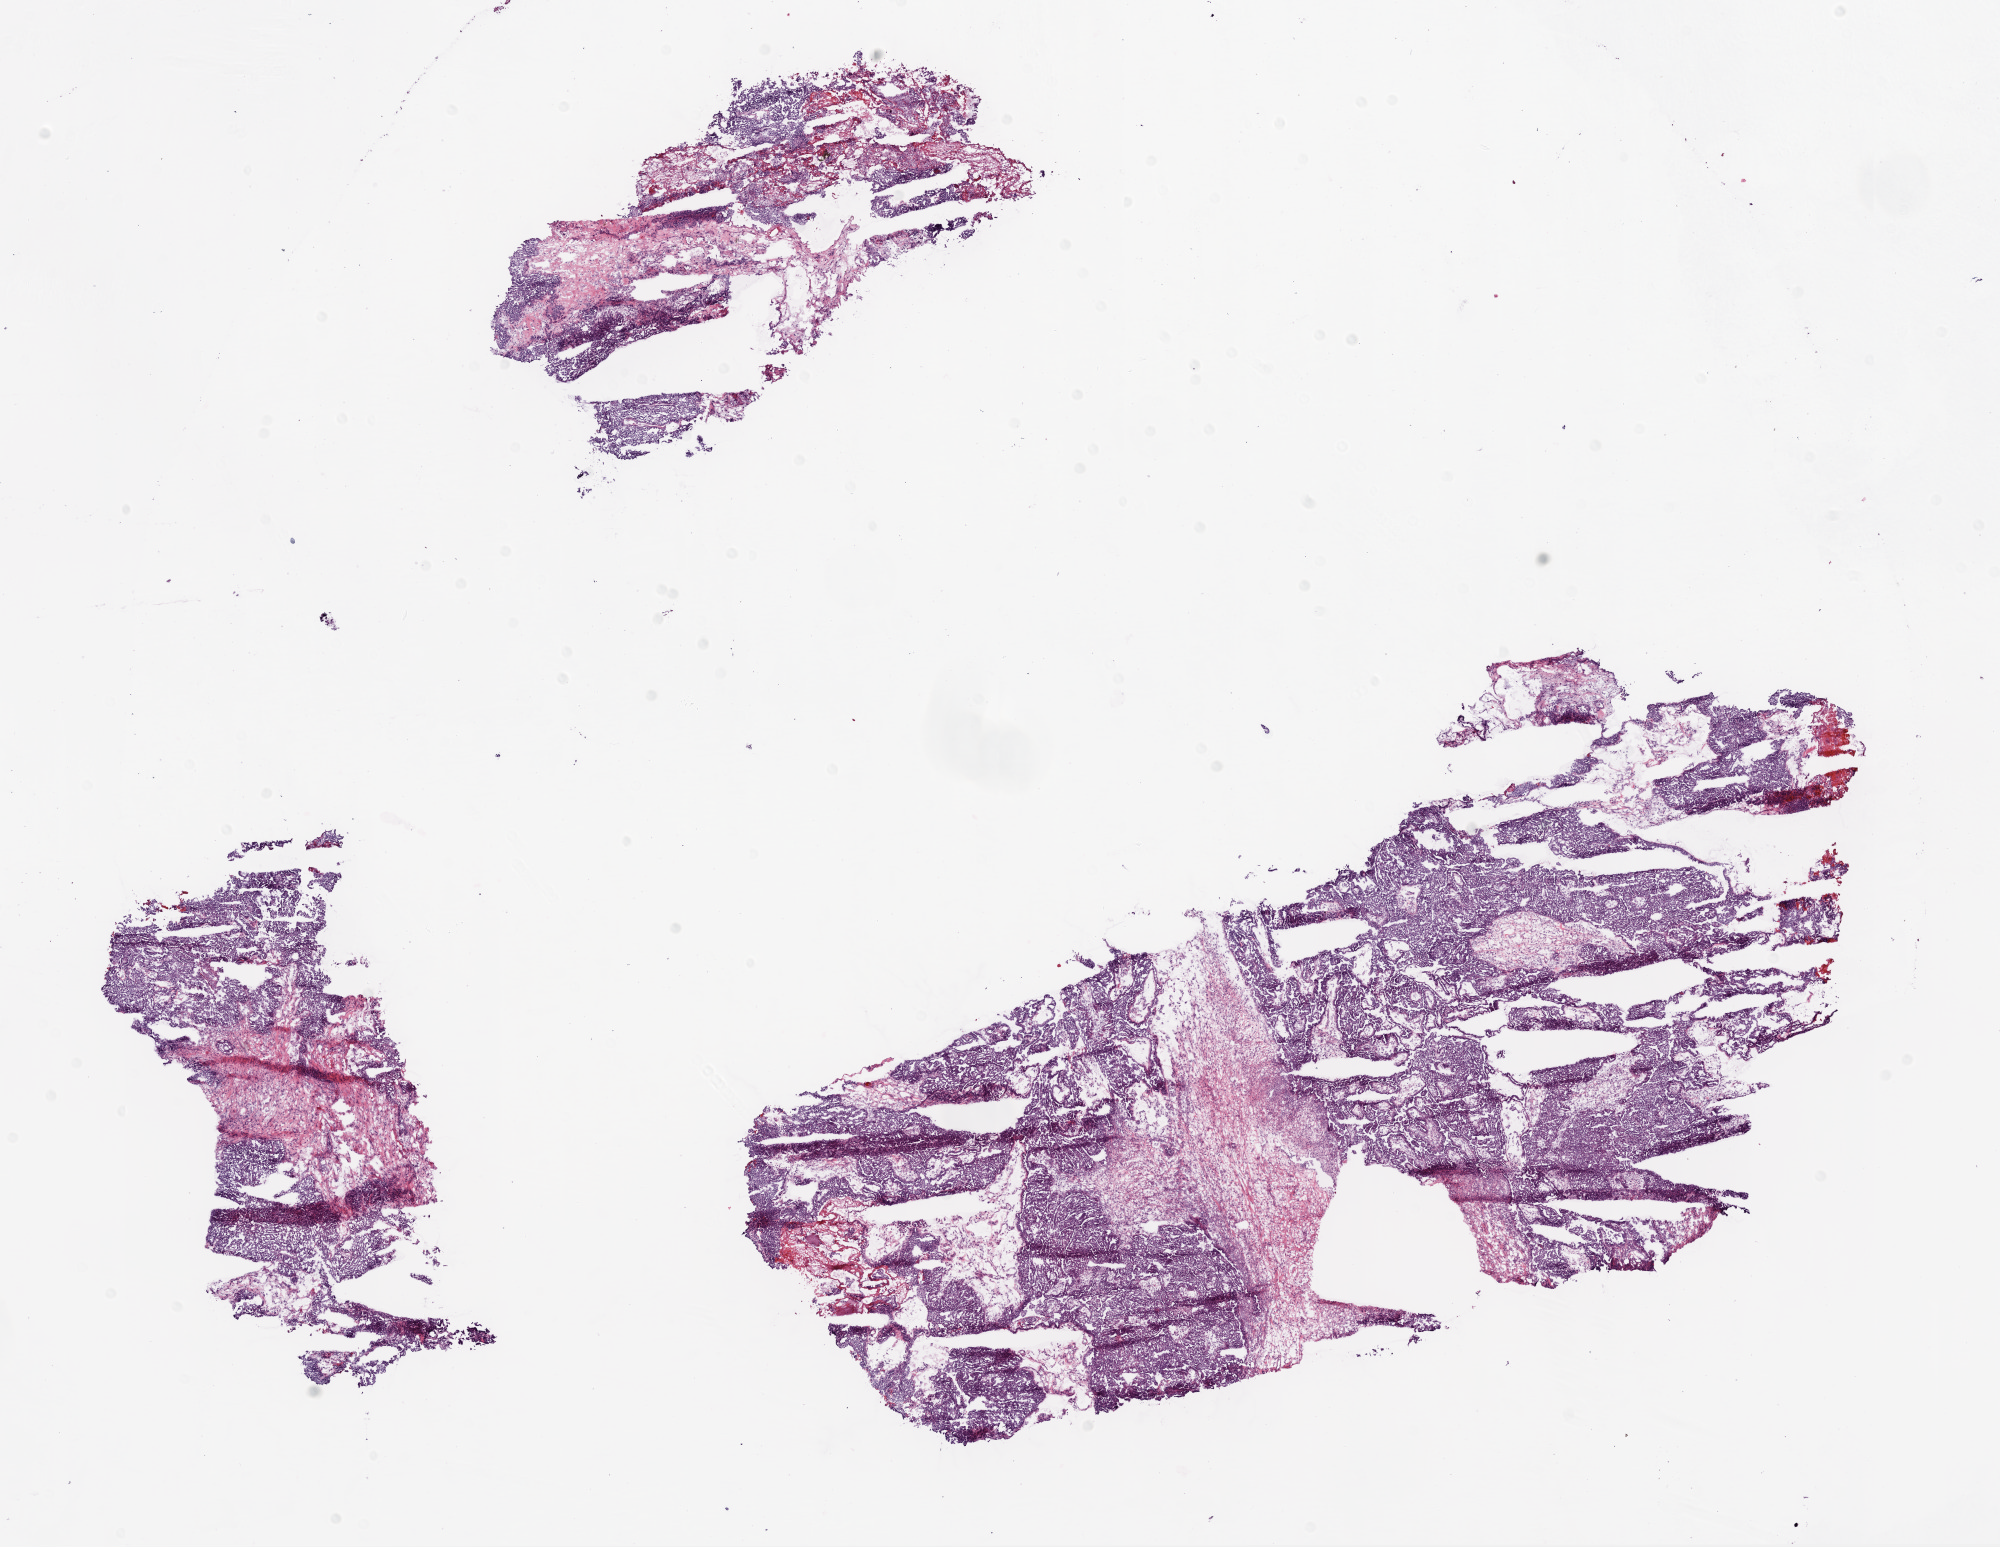
H&E-stained whole-slide image, shown as a low-resolution overview of the whole scanned area (about 16.0 x 12.4 mm, from a 20x scan), frozen section from the bottom of the tissue portion, sample: primary tumour, ovary. Female, age 58 years at initial diagnosis. Histologic grade: G3 (poorly differentiated). Slide review estimates, as recorded: tumour cells 85%, tumour nuclei 90%, normal cells 0%, stromal cells 10%, necrosis 5%.
- FIGO stage: IV
- histologic diagnosis: Serous cystadenocarcinoma, NOS
- laterality: right